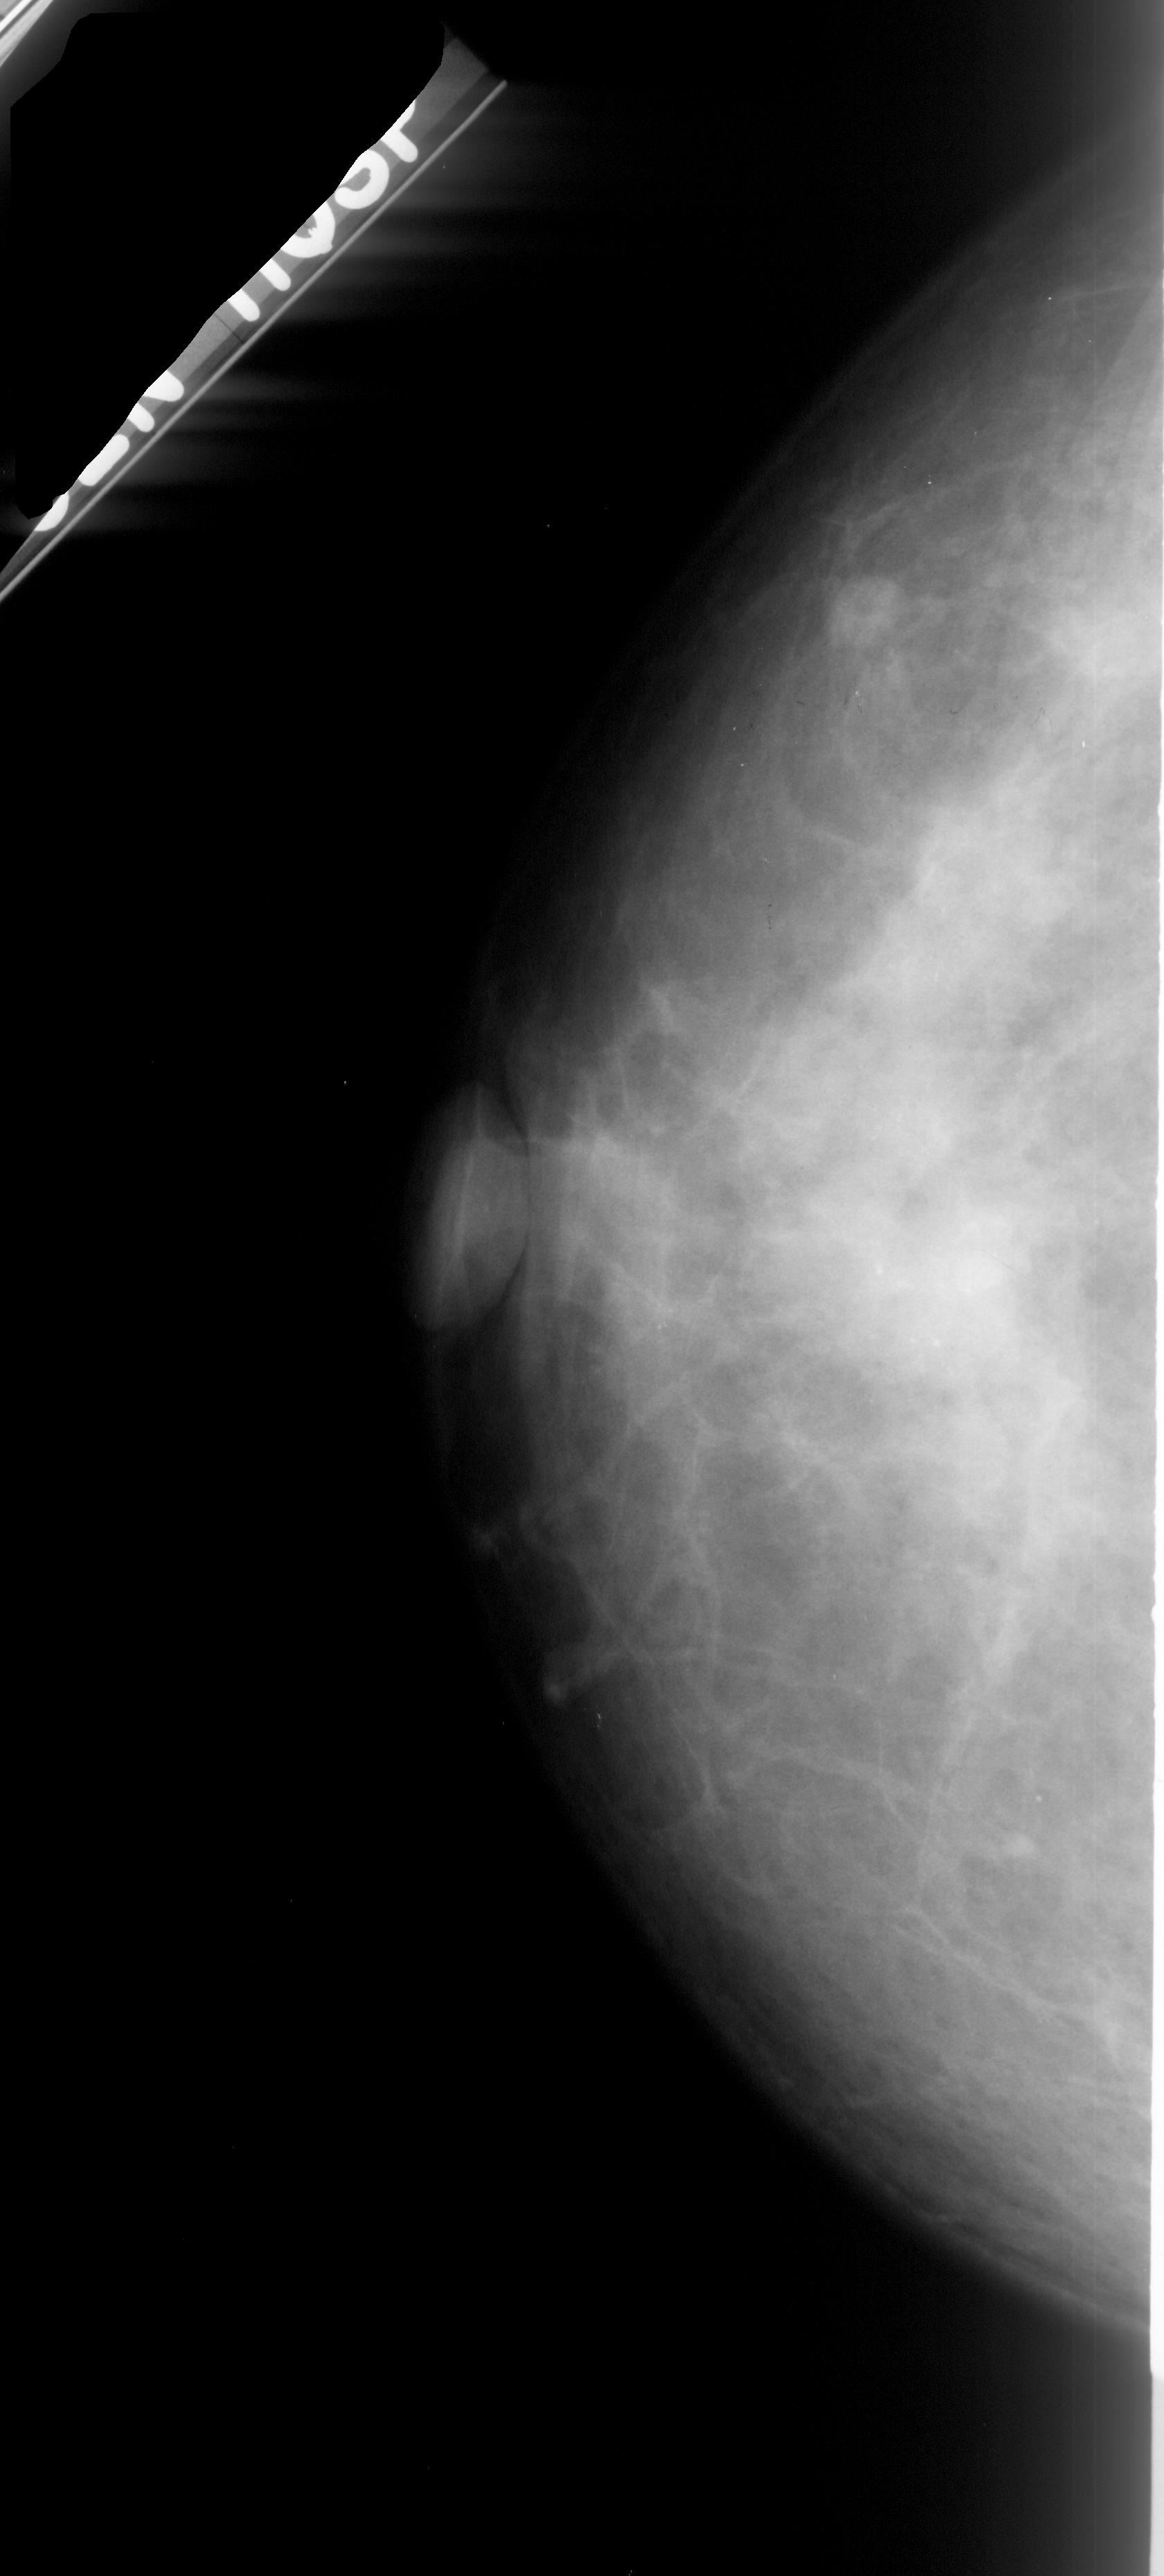
Digitized screen-film mammogram, left breast, craniocaudal (CC) view, breast composition: heterogeneously dense (BI-RADS density category 3 of 4).
Marked abnormality: calcifications, morphology pleomorphic, distribution clustered; BI-RADS assessment category 4; subtlety rating 2 on a 1 (subtle) to 5 (obvious) scale; pathology (as recorded): malignant.